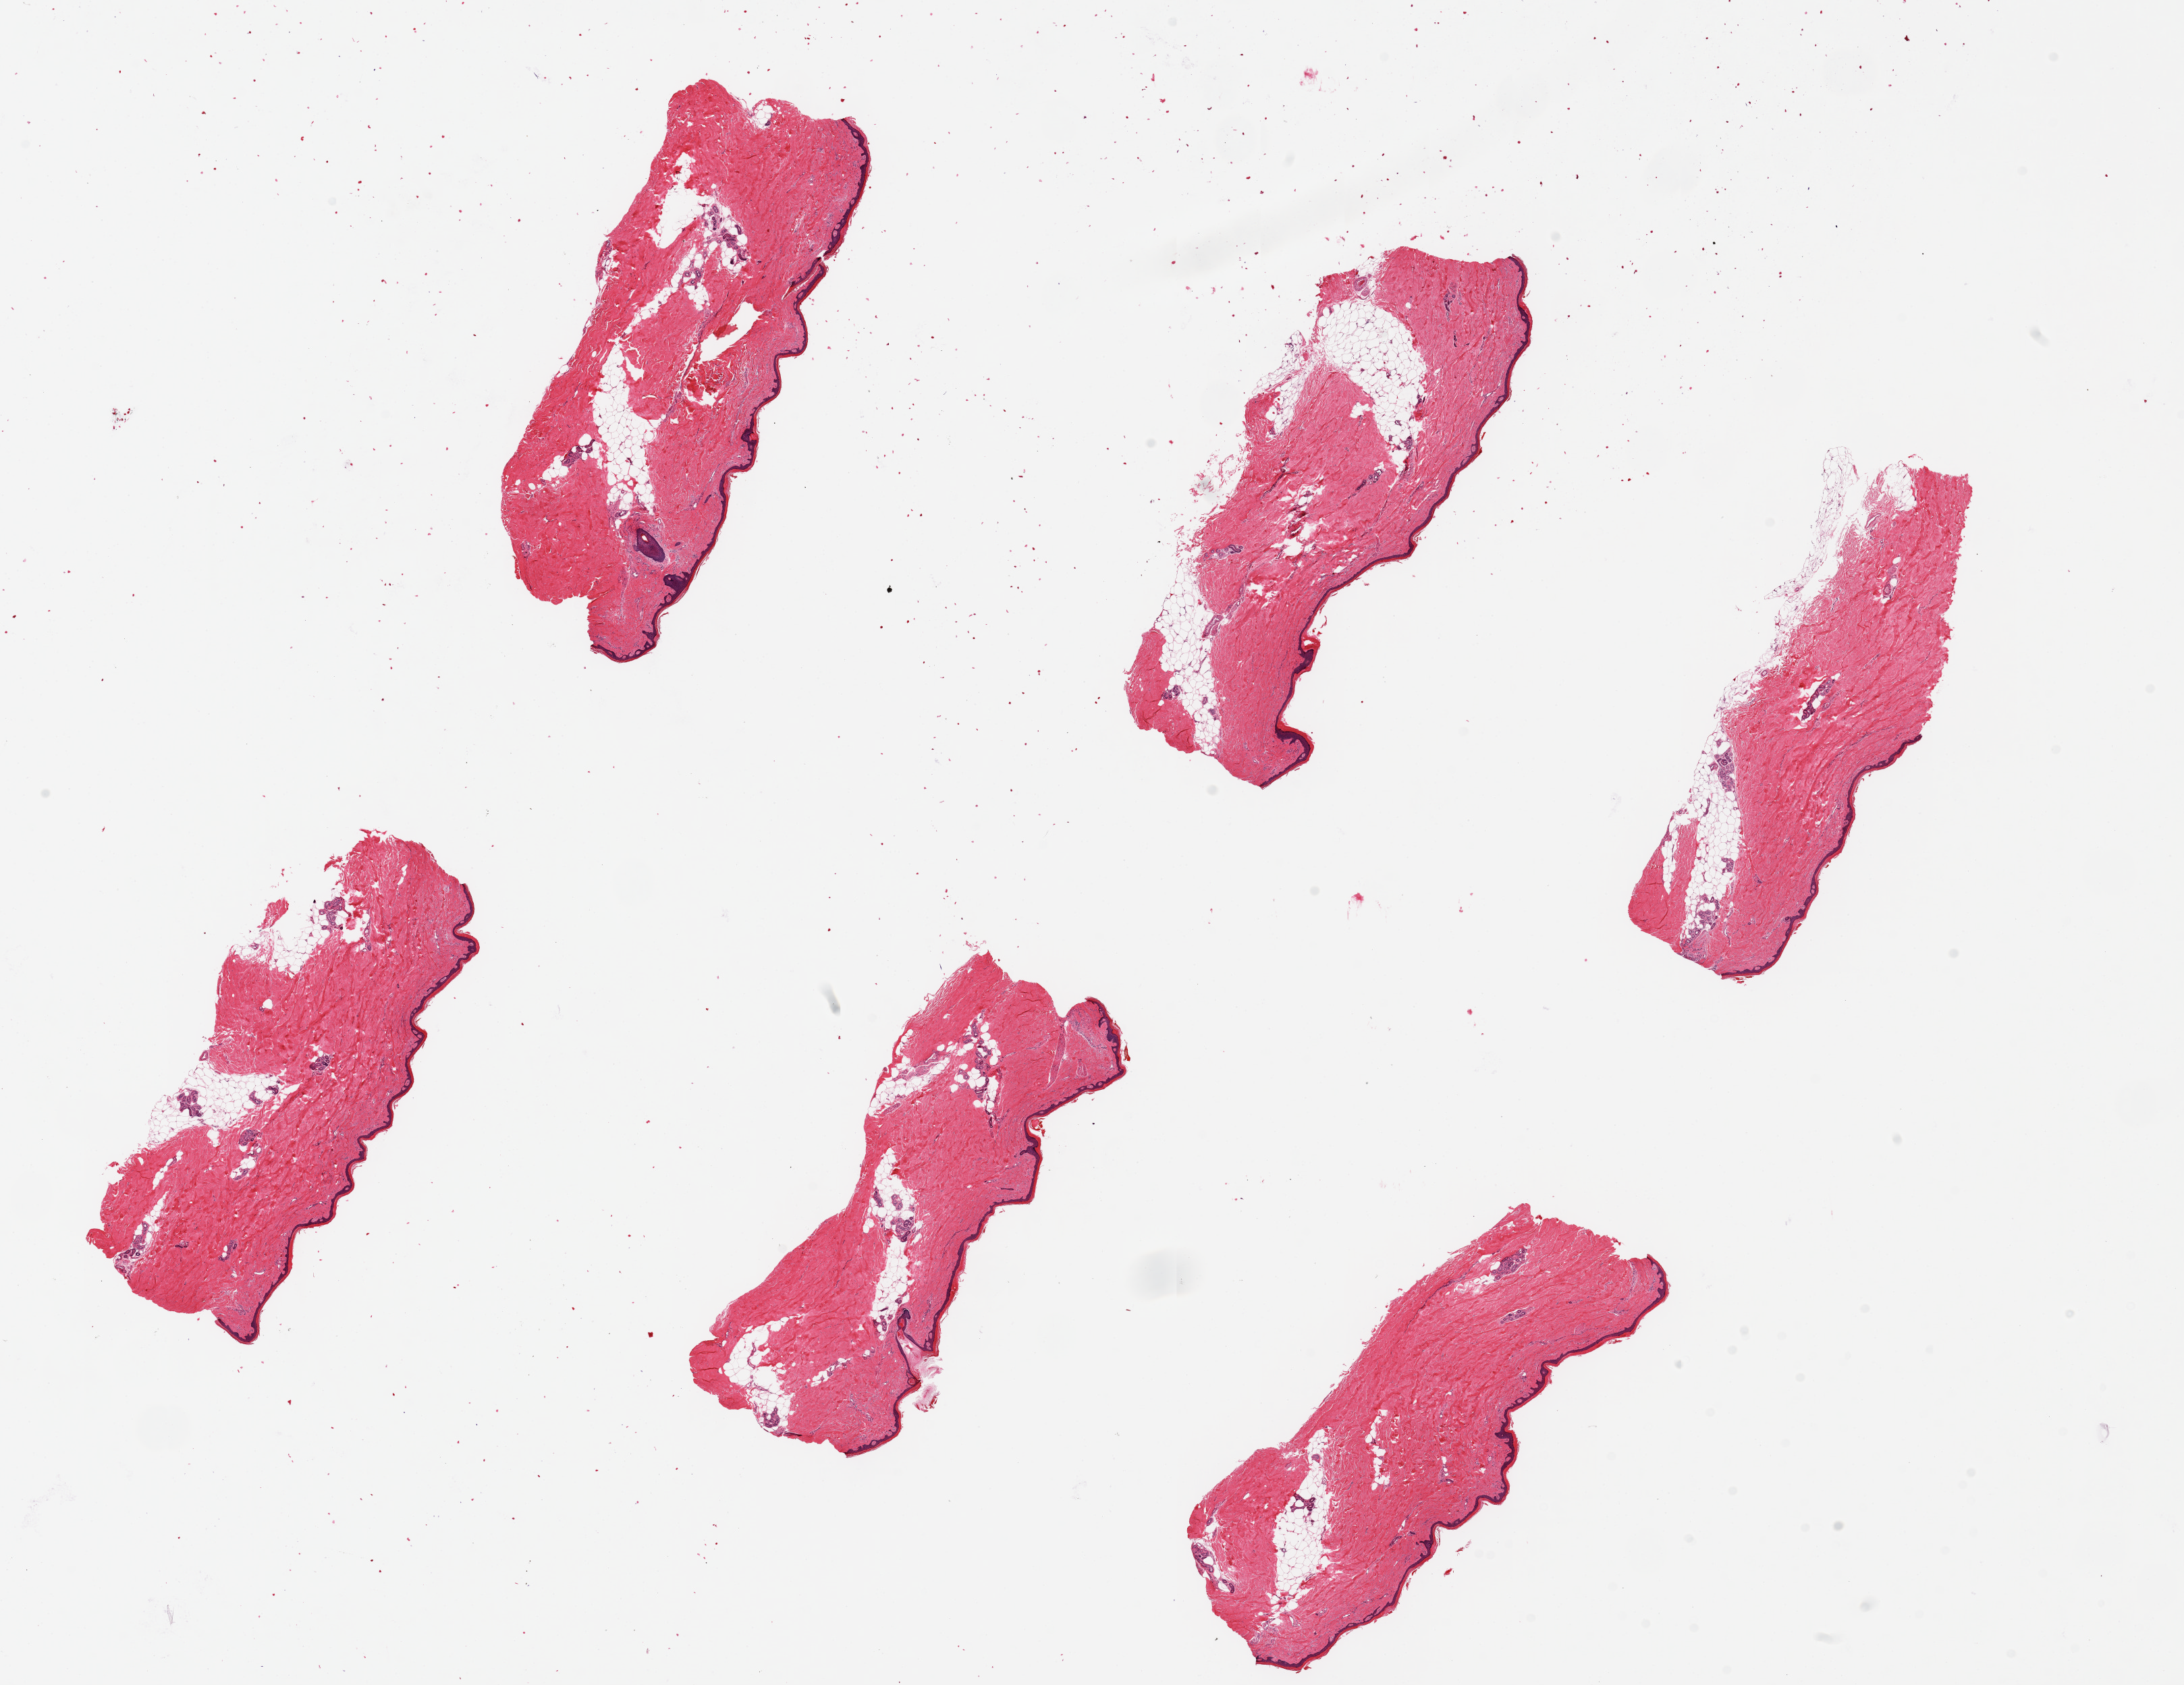
Digitized haematoxylin and eosin-stained section, shown as a low-resolution overview of the whole scanned area (about 25.6 x 19.7 mm). PAXgene-fixed, paraffin-embedded tissue. Section of skin of lower leg (target tissue). Donor tissue sample. Male donor.
Review note (as recorded): 6 pieces, up to 7x3mm; Well trimmed, no subcutaneous adipose, but internal adipose is up to 30%.